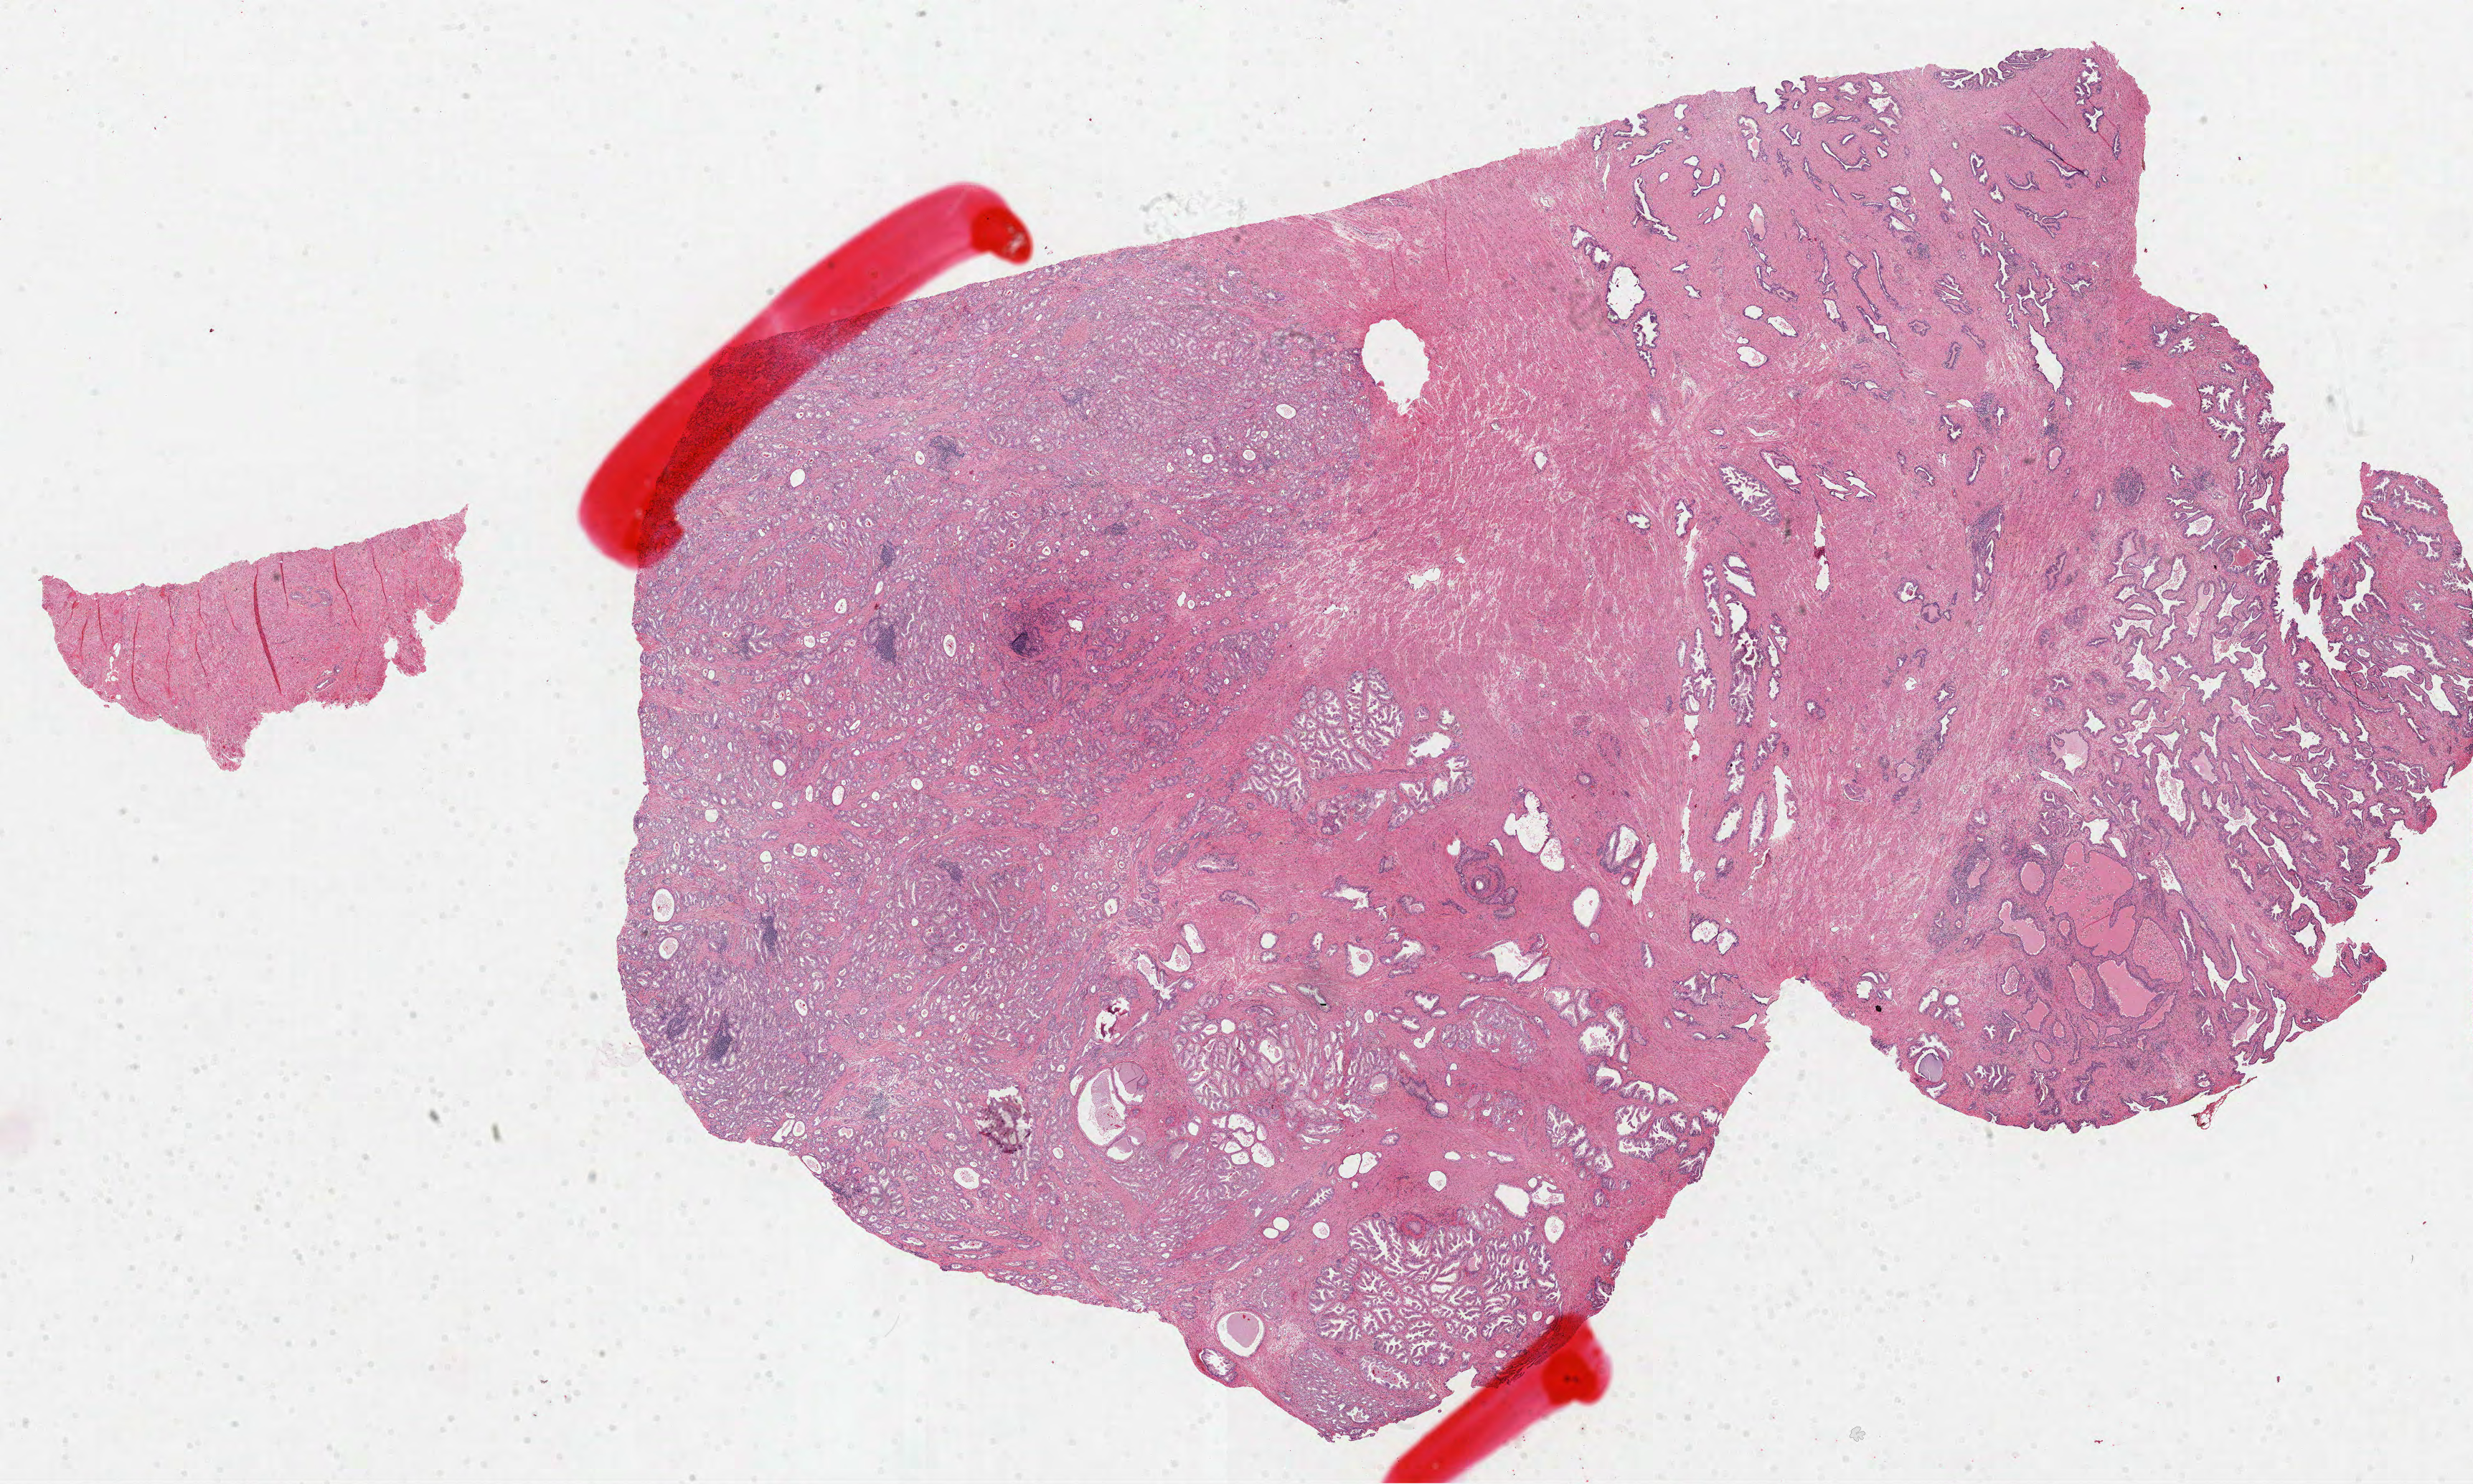
Whole-slide histology image, H&E-stained, a low-resolution overview of the entire scanned area, about 27.8 x 16.7 mm. Formalin-fixed paraffin-embedded (FFPE) diagnostic section. Primary tumour sample from the prostate. Patient: male, age at initial diagnosis 55 years. Gleason score: 6 (3+3).
• diagnosis: Acinar cell carcinoma (prostate gland)